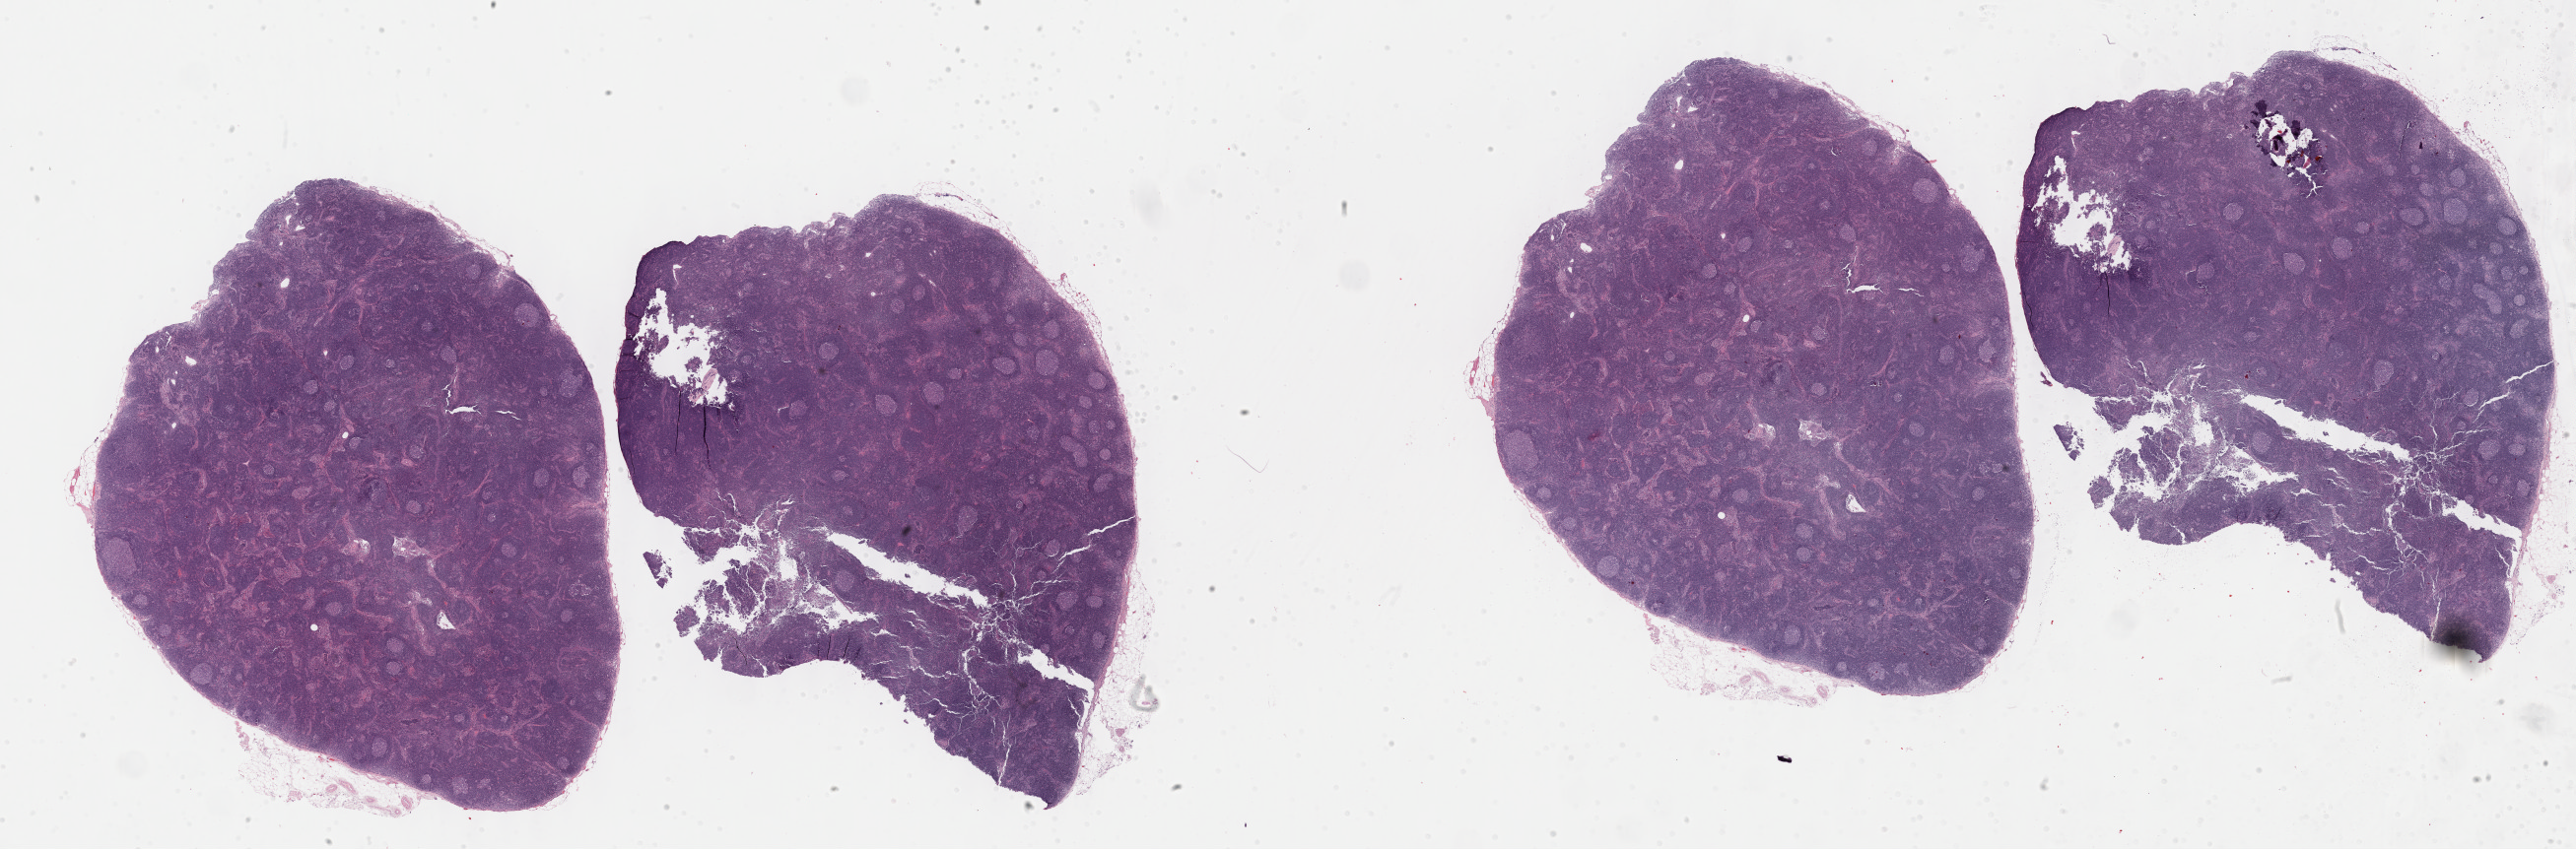
Digitized Hematoxylin and eosin (H&E) stained tissue section (whole slide), shown as a low-resolution overview of the whole scanned area (about 42.3 x 13.9 mm), FFPE section, primary tumour sample from the skin. Male patient; age at initial diagnosis 56 years.
• diagnosis: Malignant melanoma, NOS